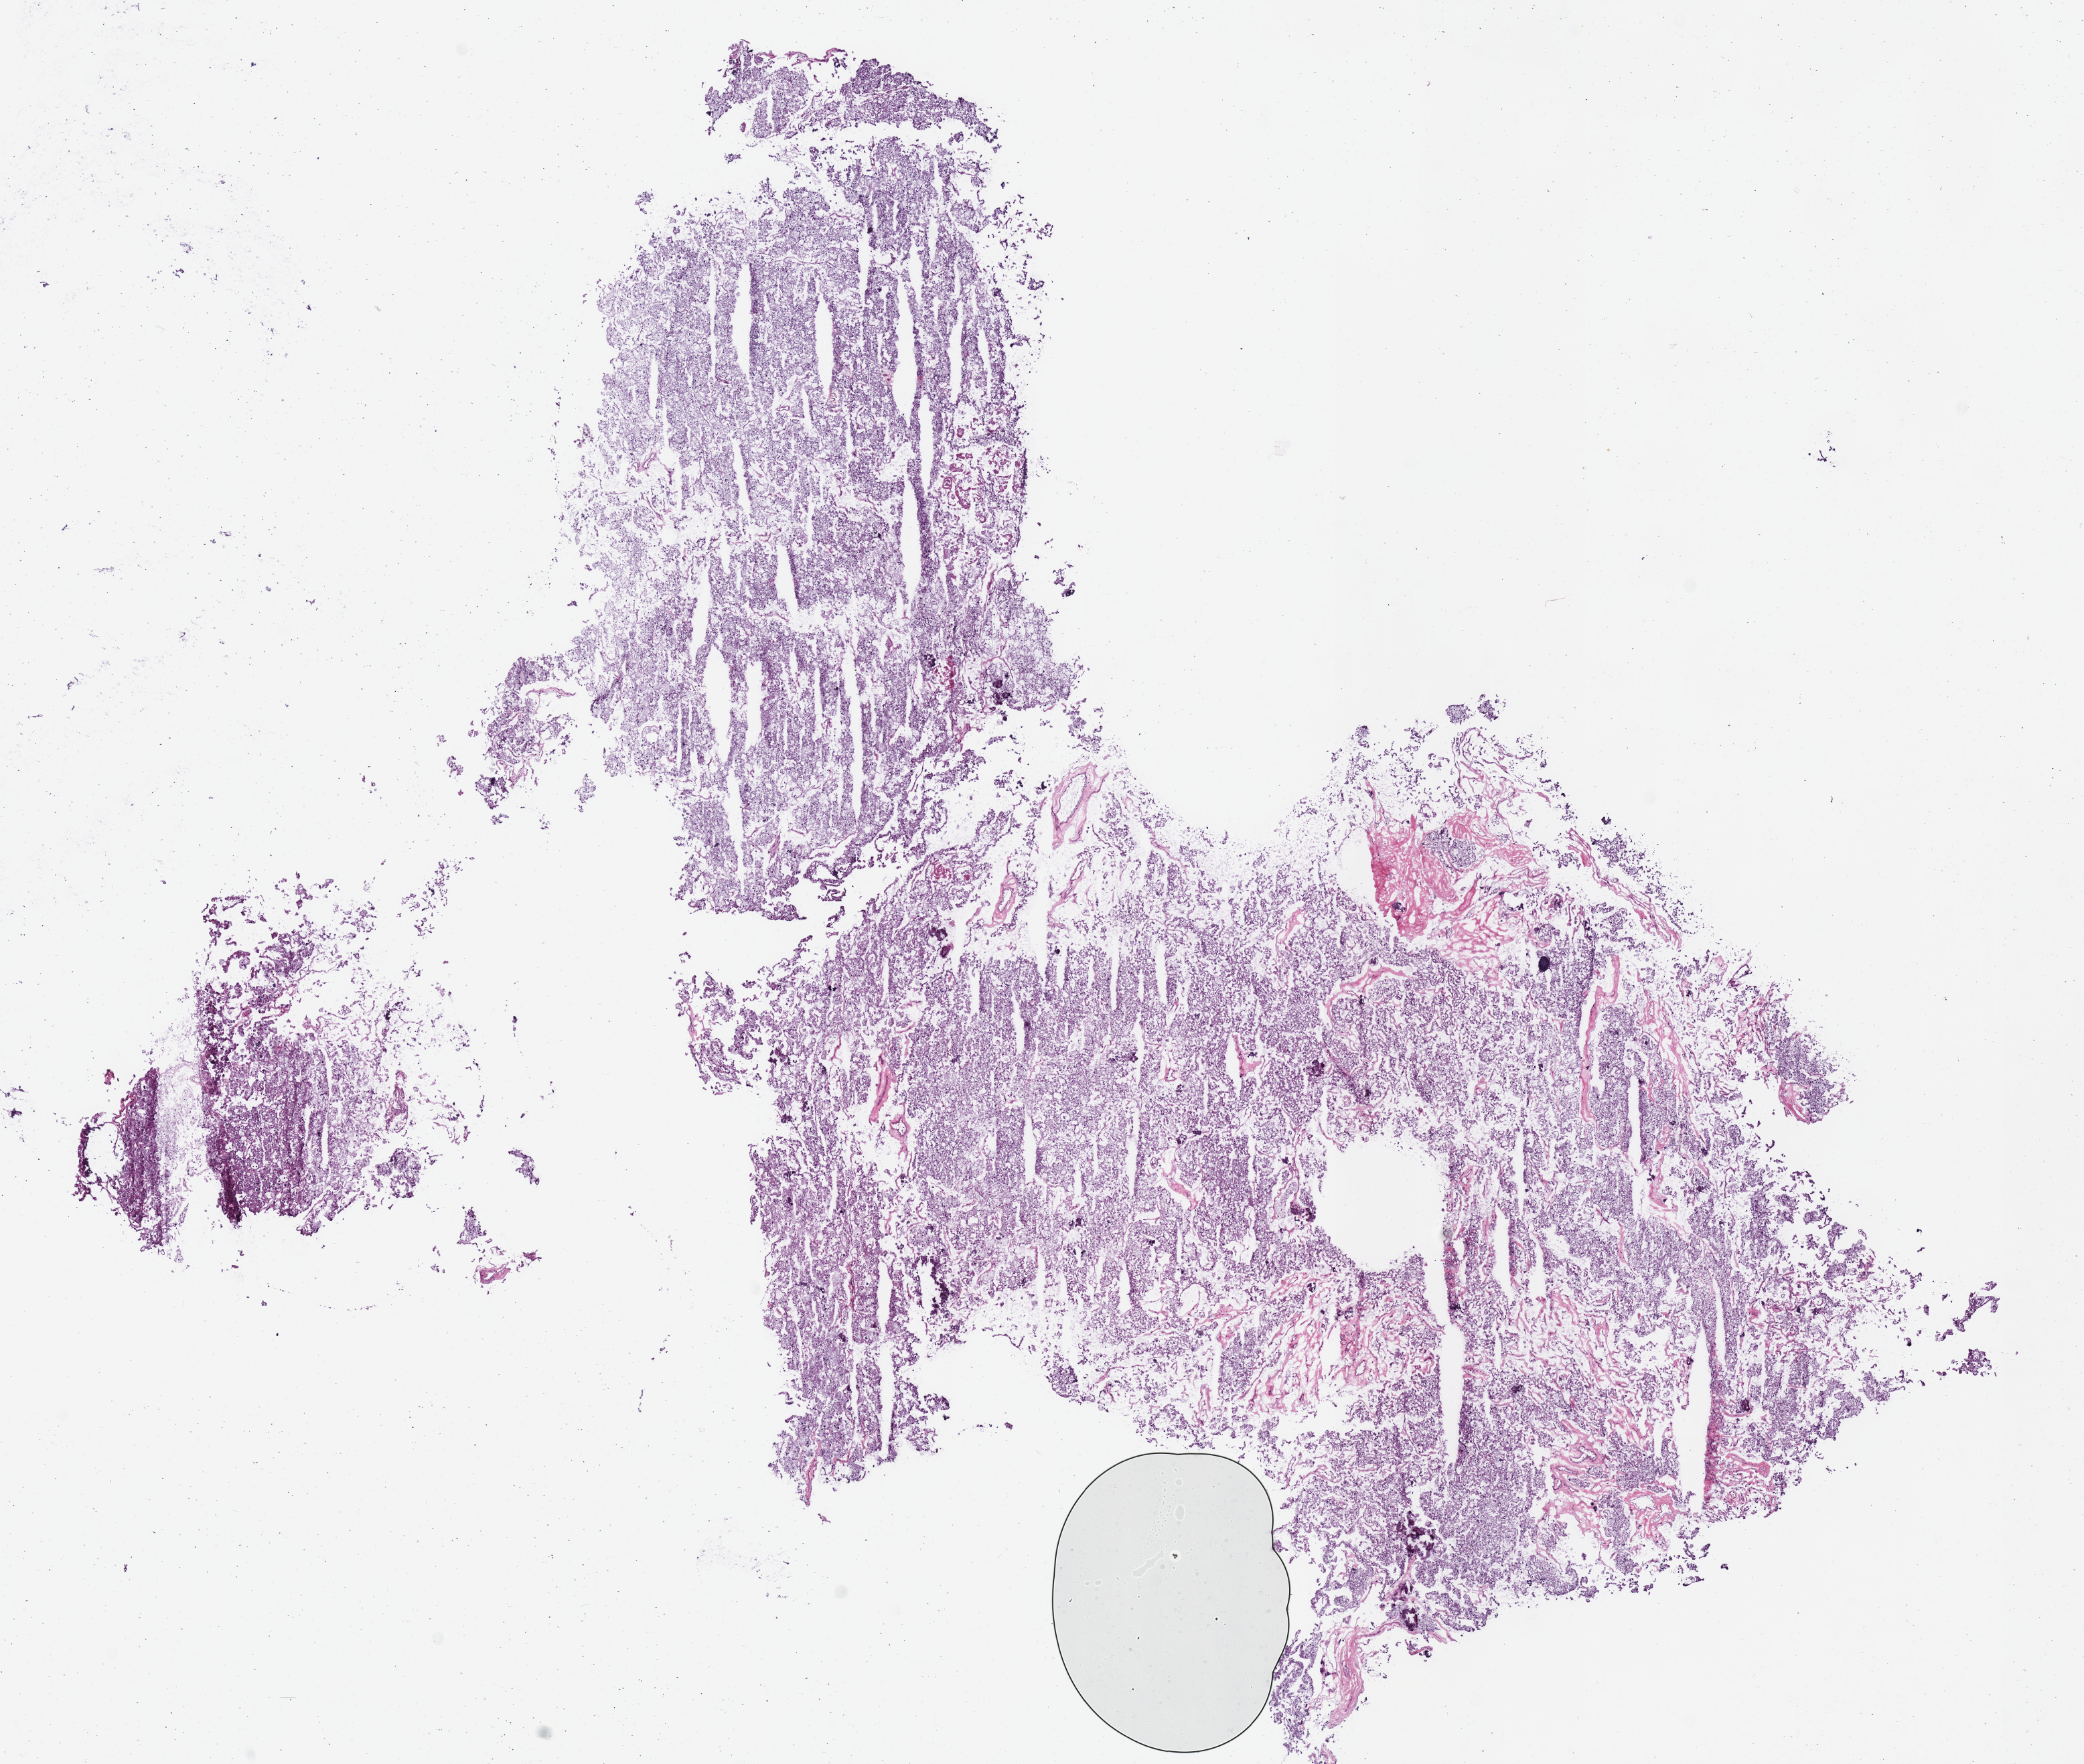
Digitized Hematoxylin and eosin (H&E) stained tissue section (whole slide) — low-resolution overview of the scanned area, about 12.2 x 10.4 mm (slide scanned at 40x); frozen section from the top of the tissue portion; sample: primary tumour, kidney. Patient: male, age at initial diagnosis 47 years. Pathologist review of this section (percent, as recorded): tumour cells 92%, tumour nuclei 90%, normal cells 0%, stromal cells 8%, necrosis 0%.
Diagnosis: Renal cell carcinoma, chromophobe type. AJCC pathologic stage: I (5th edition).